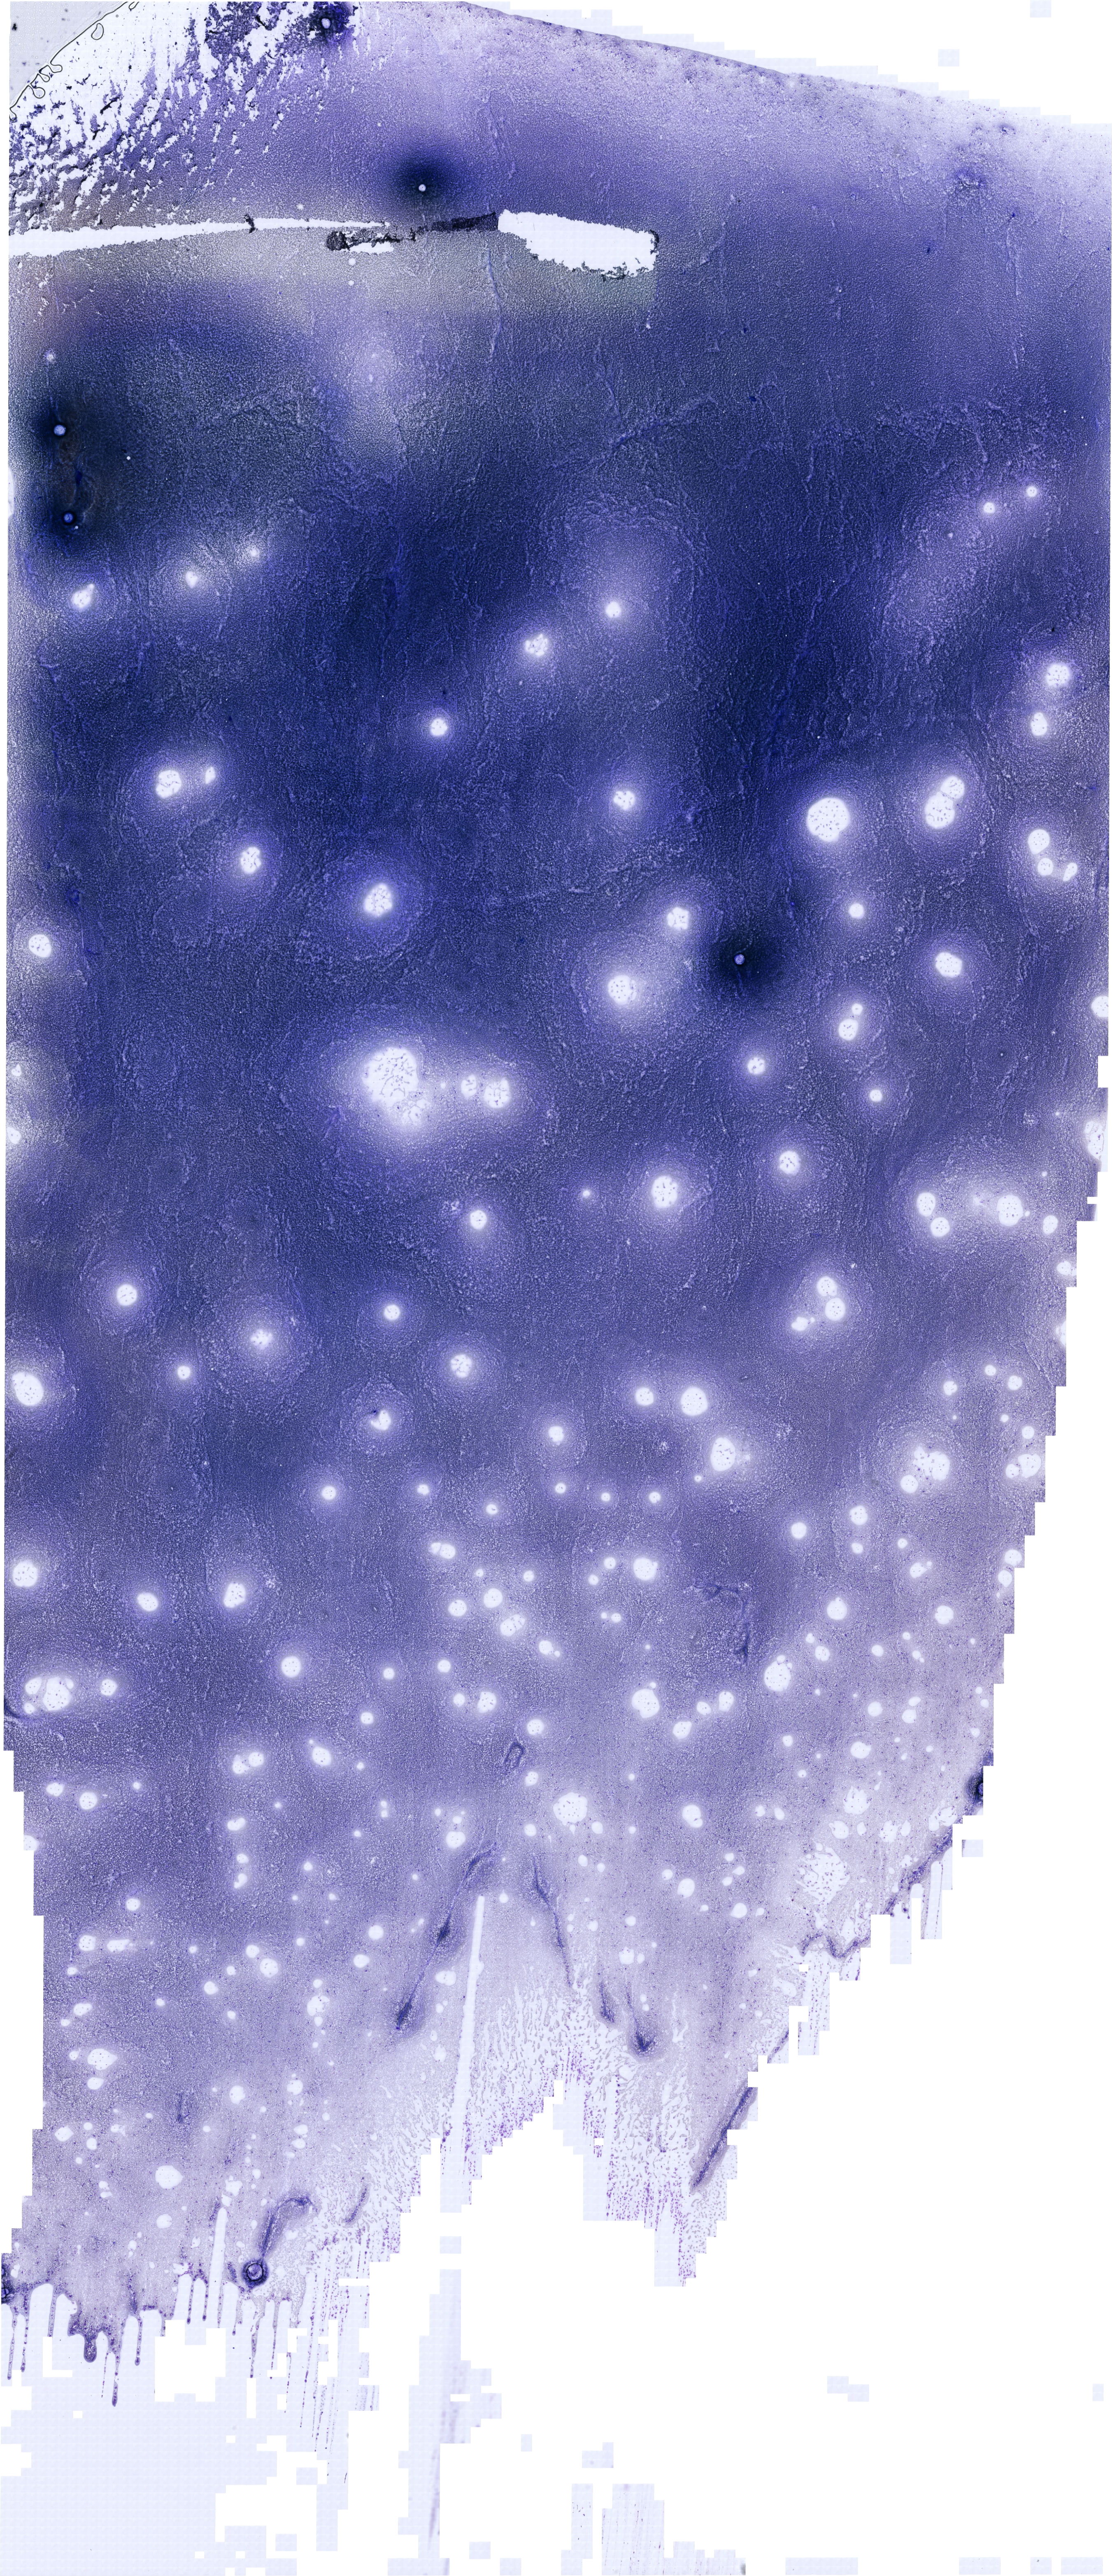
Whole-slide image of a May-Grünwald-Giemsa (MGG)-stained bone marrow aspirate smear — a low-resolution overview of the entire scanned area, about 21.1 x 48.9 mm. Patient sex: female.
- diagnosis: Burkitt Leukemia